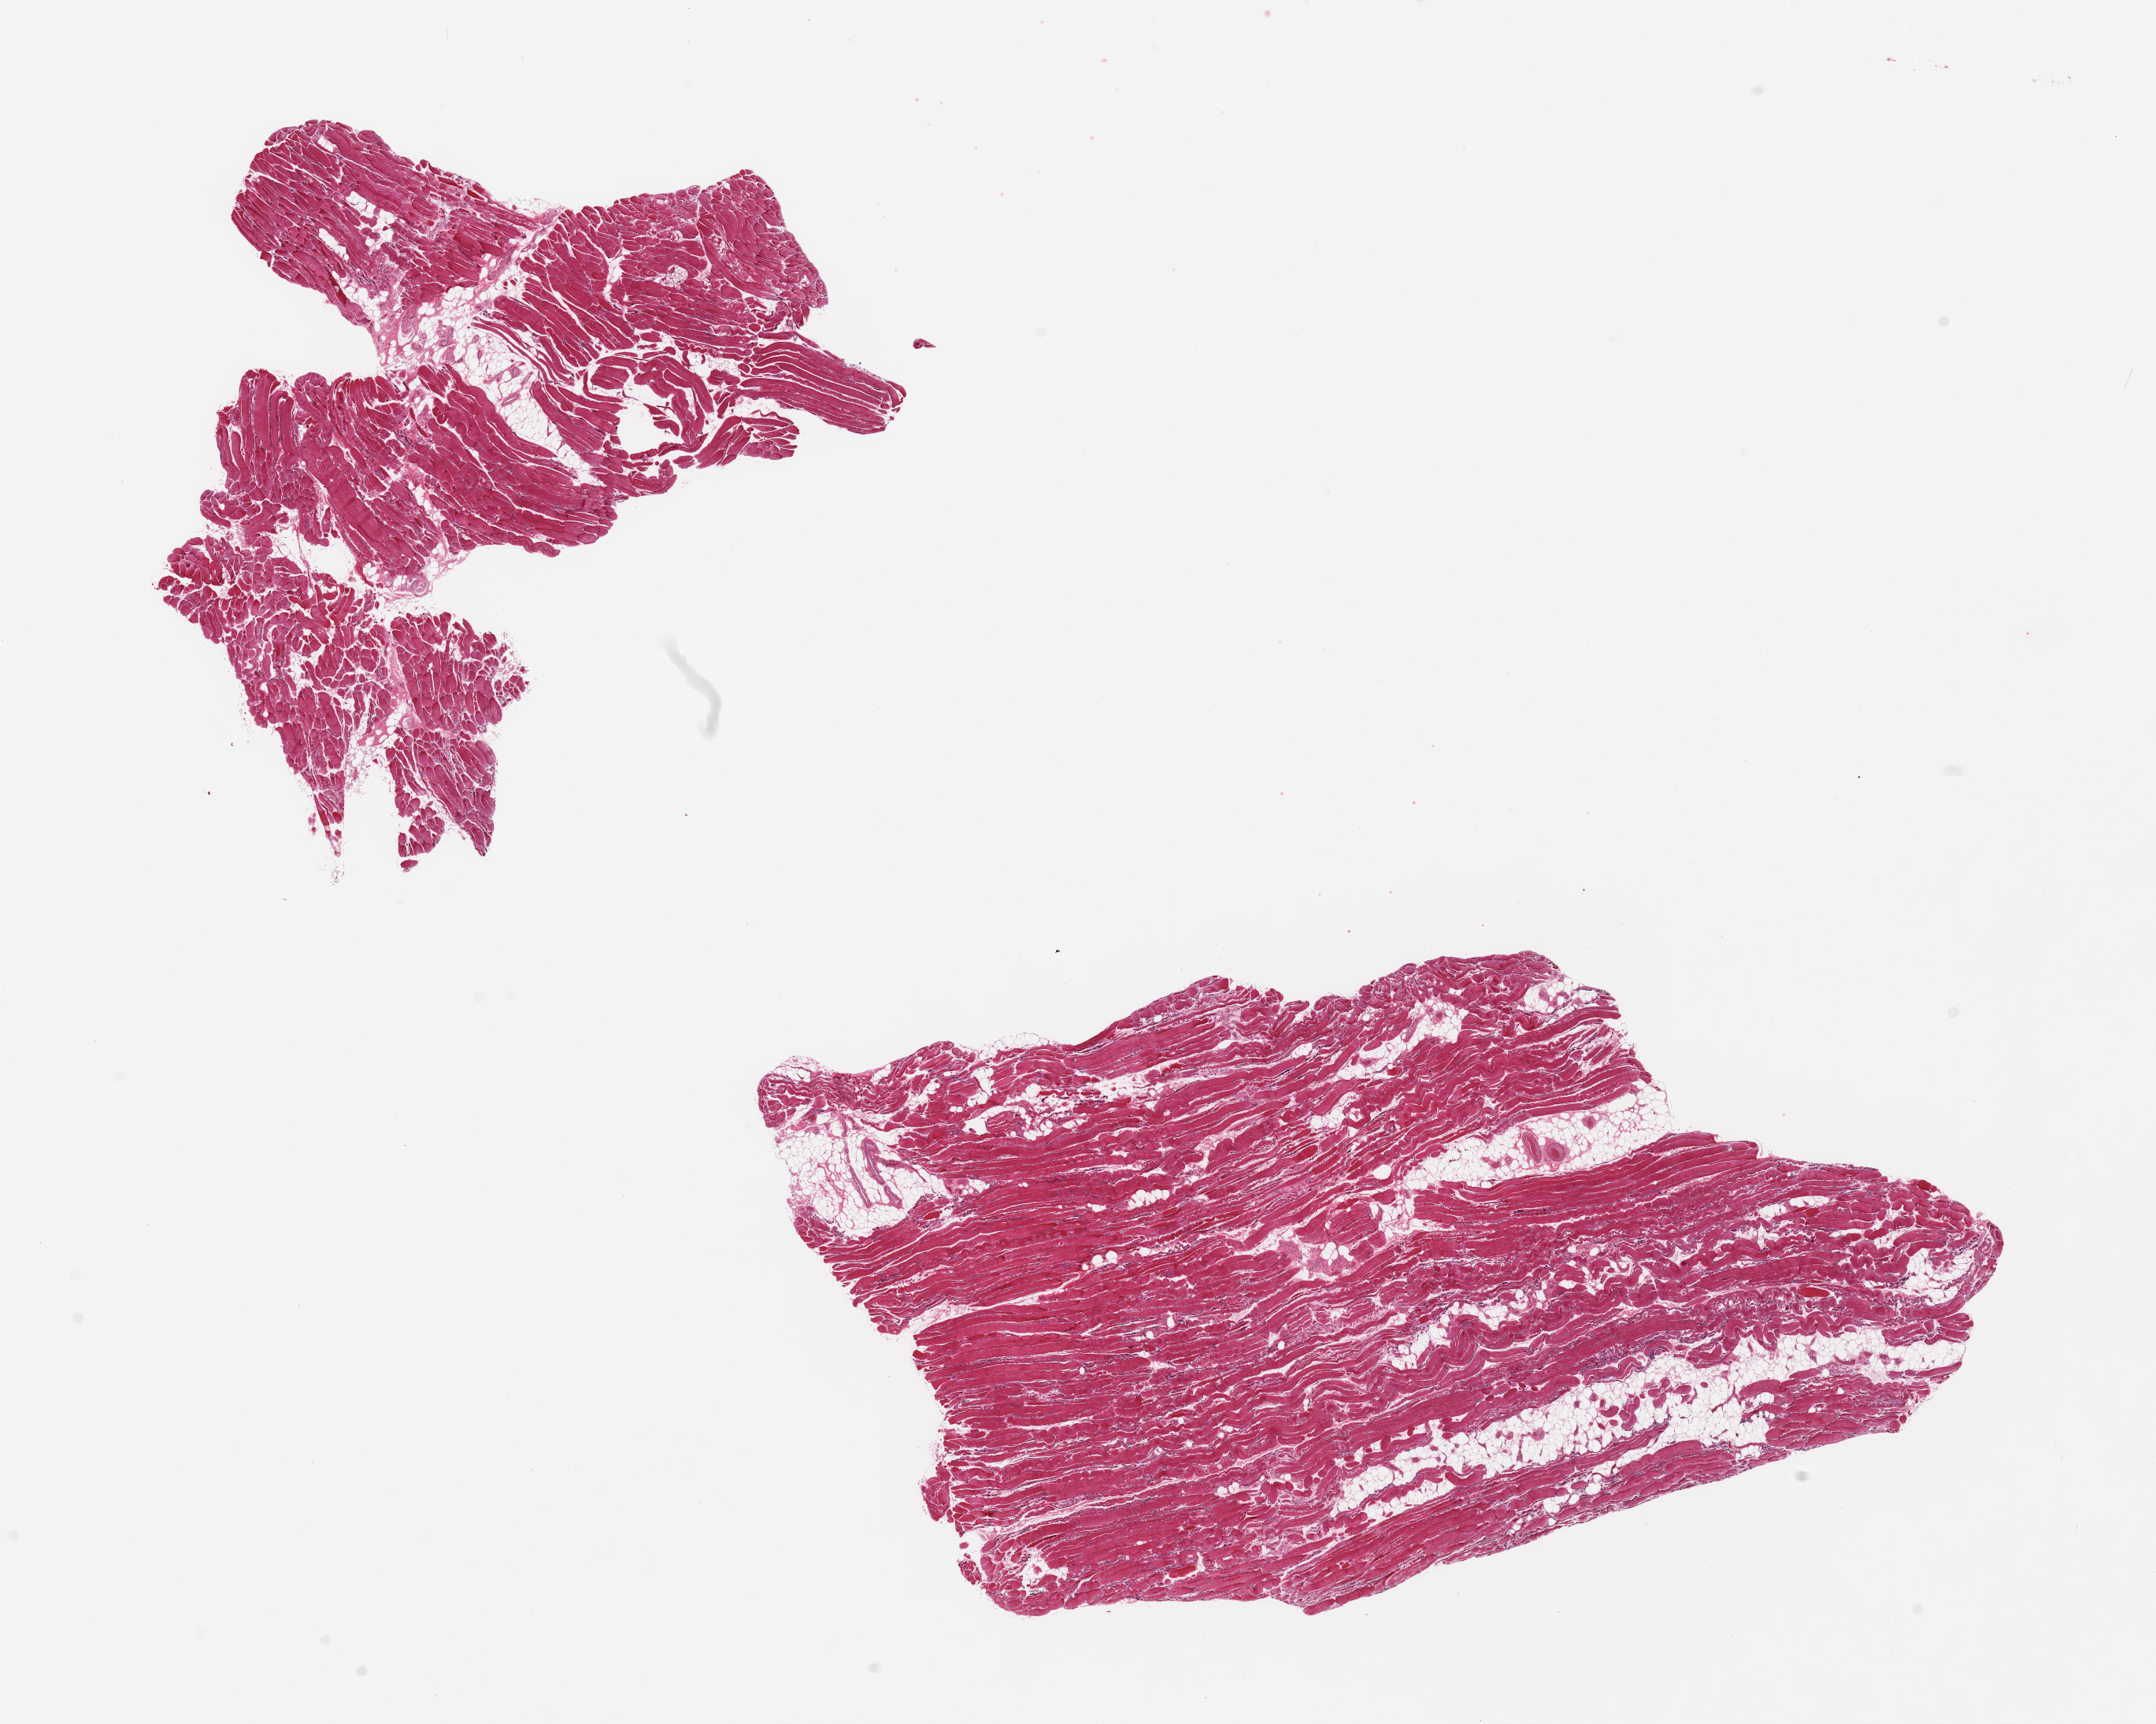
Haematoxylin and eosin whole-slide image, low-resolution overview of the scanned area, about 21.7 x 17.3 mm (acquisition: 20x scan), PAXgene-fixed paraffin-embedded (PFPE) section, section of skeletal muscle (target tissue), tissue donor sample. Female donor.
Reviewer comment on this tissue sample: 2 pieces; moderate atrophy; 20 & 10% internal fat.